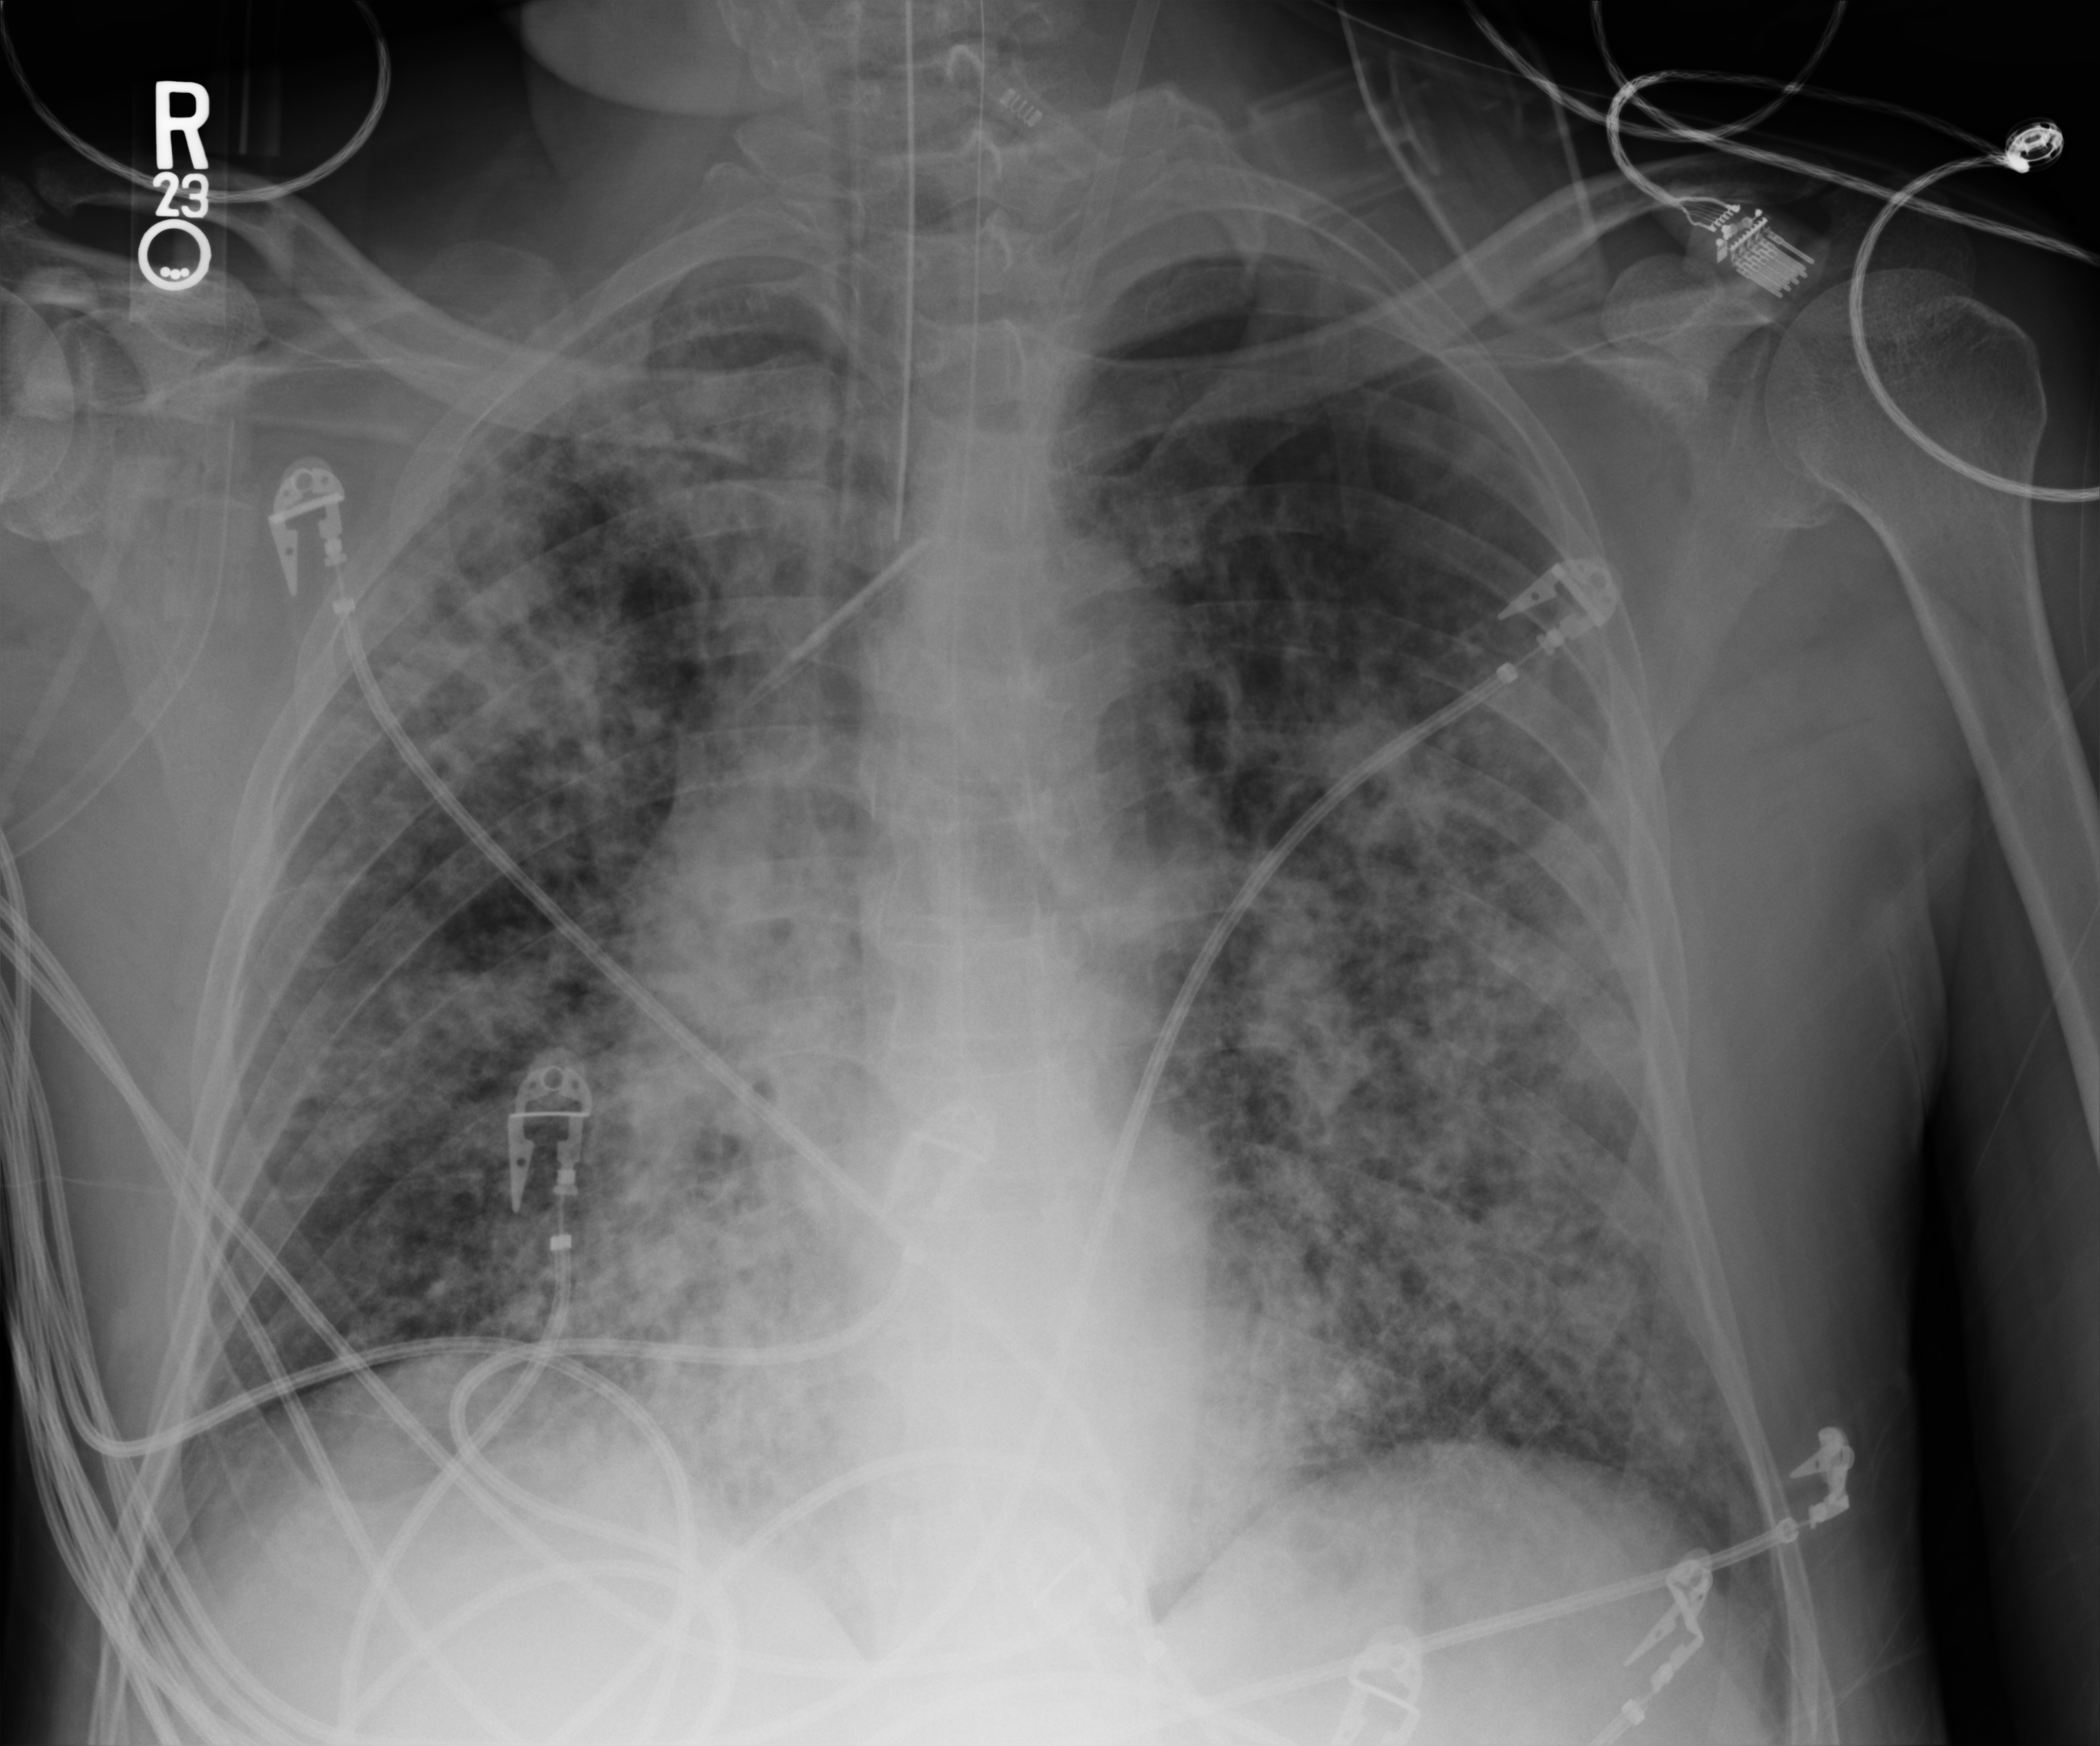
Chest X-ray (portable), anteroposterior (AP) projection. Patient hospitalised with COVID-19; male, aged 60–74 years.
Admission-level facts for this patient (not findings on this image; timing relative to this image not recorded): admitted to intensive care during this hospital stay: yes; mechanically ventilated during this hospital stay: yes.